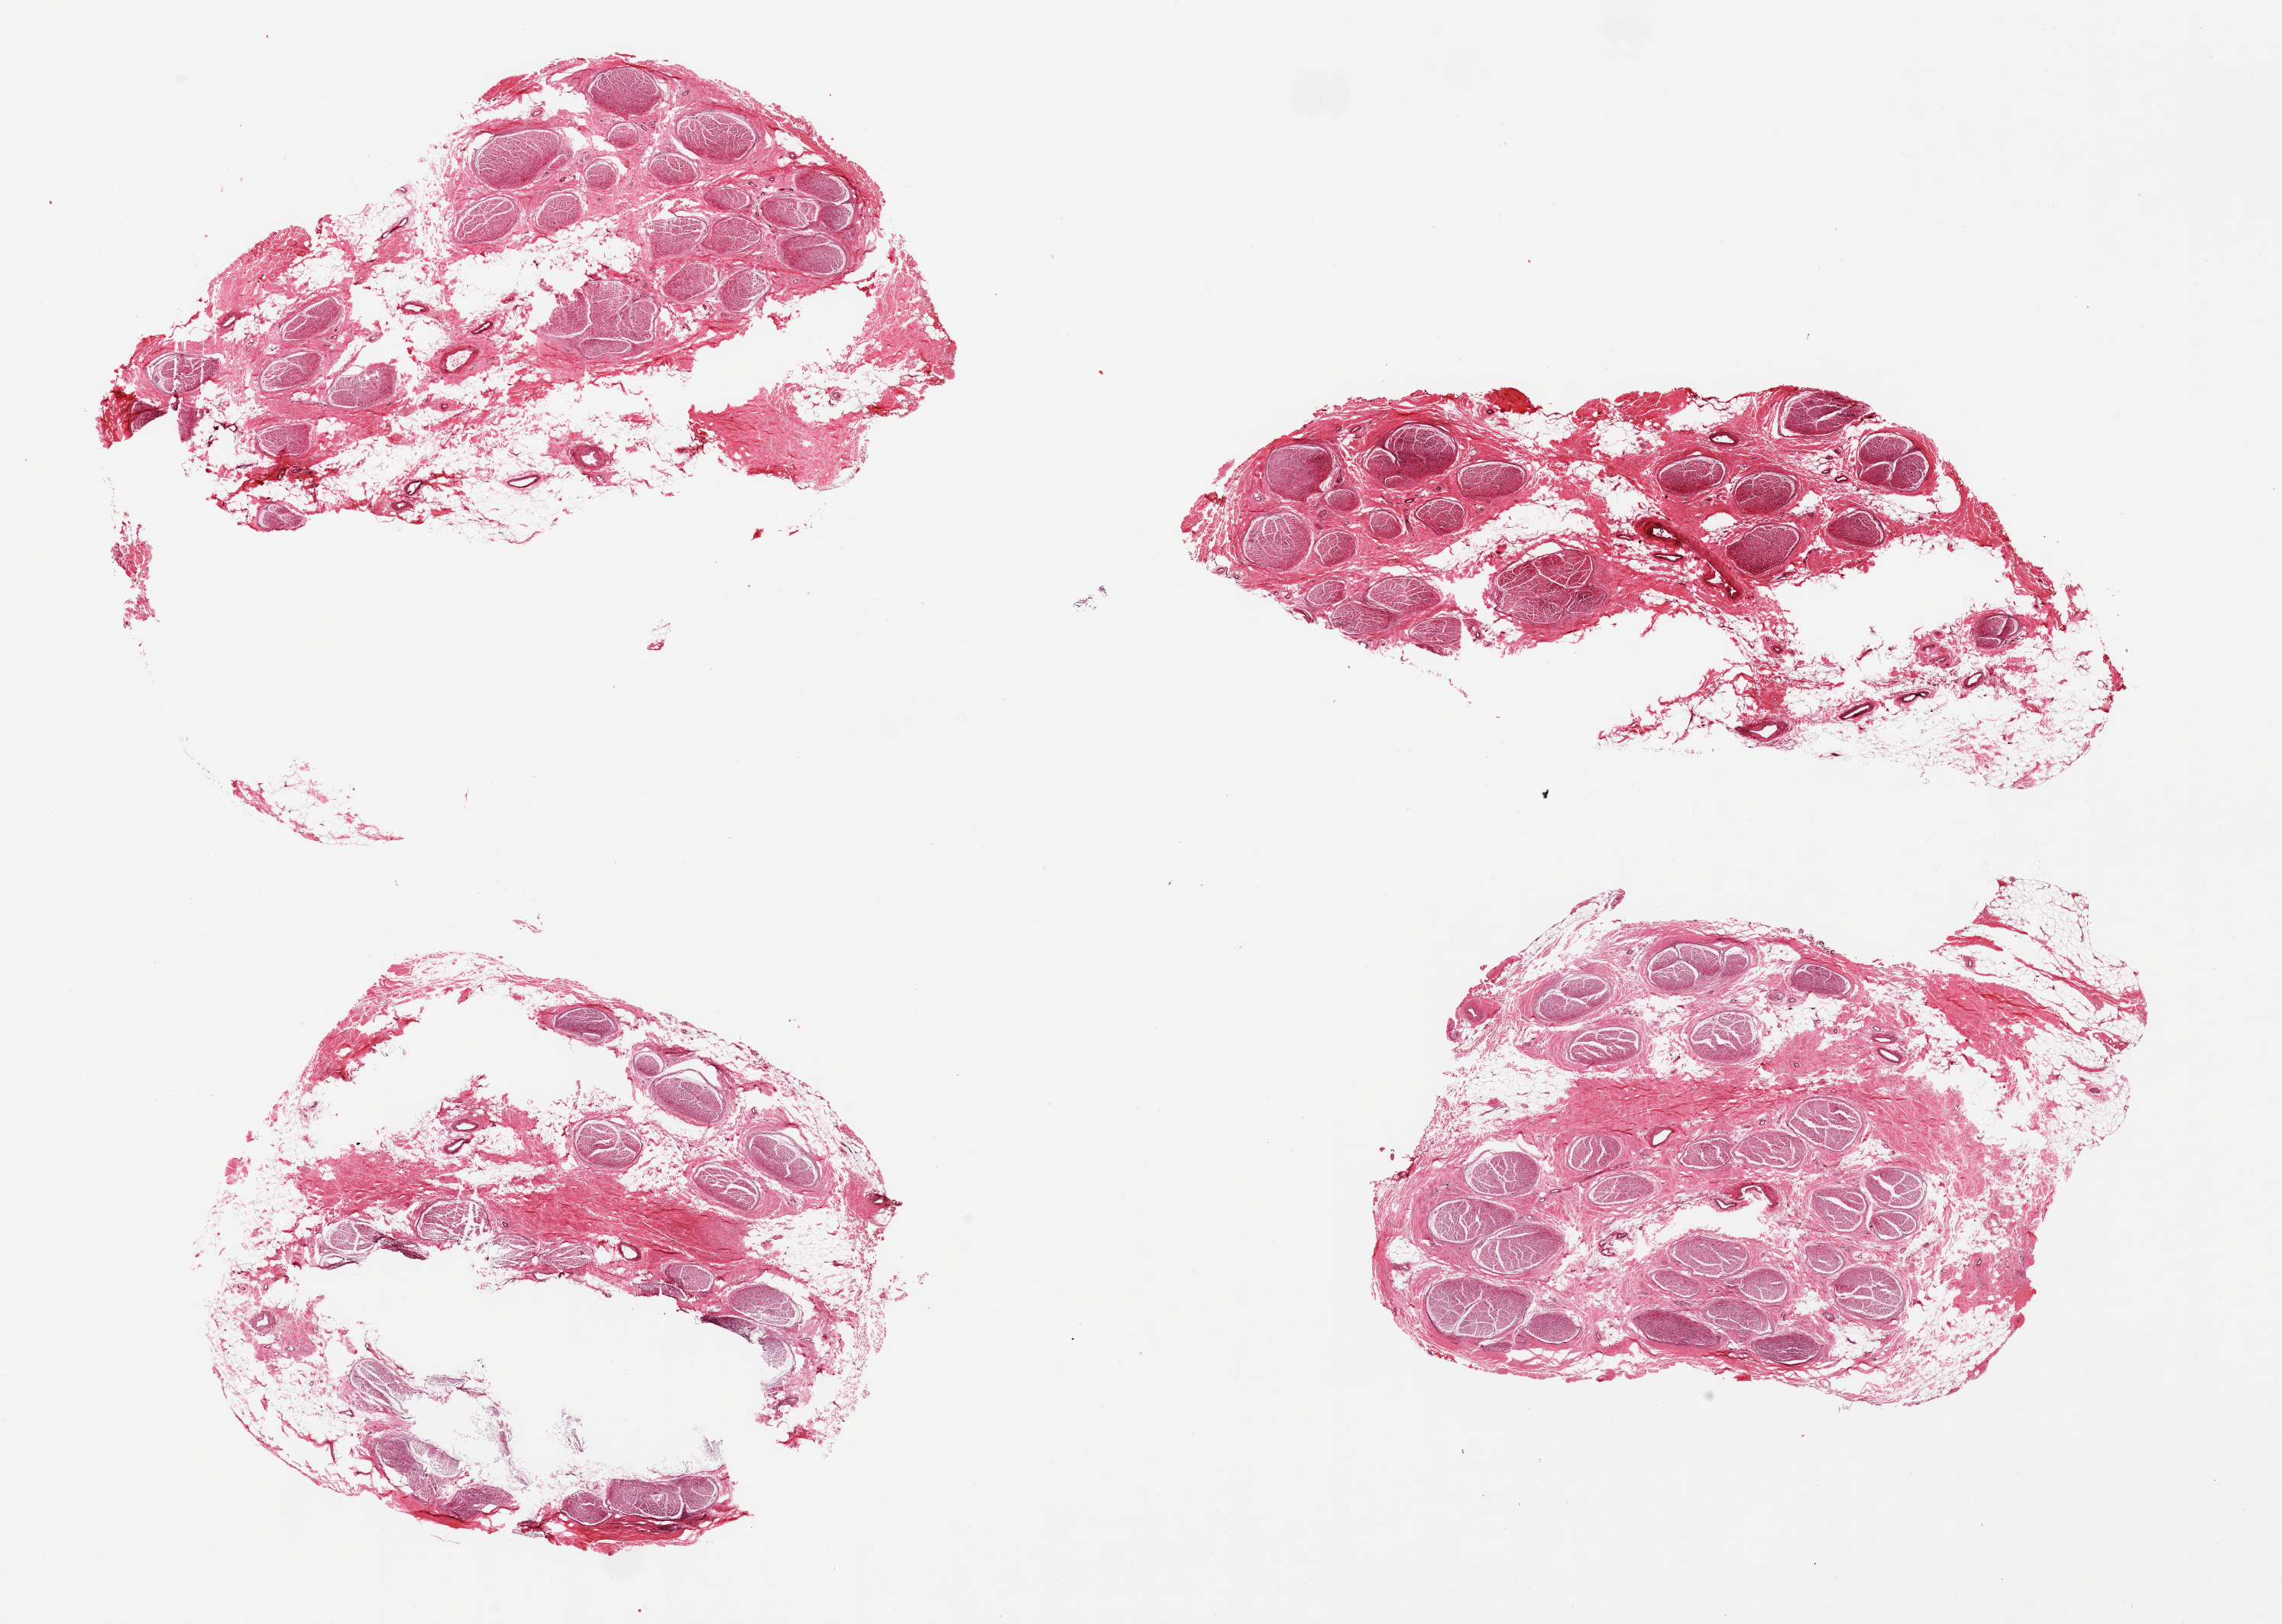
H&E whole-slide image — low-resolution overview of the scanned area, about 23.6 x 16.8 mm (slide scanned at 20x). PAXgene-fixed paraffin-embedded (PFPE) section. Section of tibial nerve (target tissue). Donor tissue sample. Donor: male.
Reviewer comment on this tissue sample: 4 pieces. 3 of 4 pieces have large central holes, possibly related to unfixed or fractured fat.